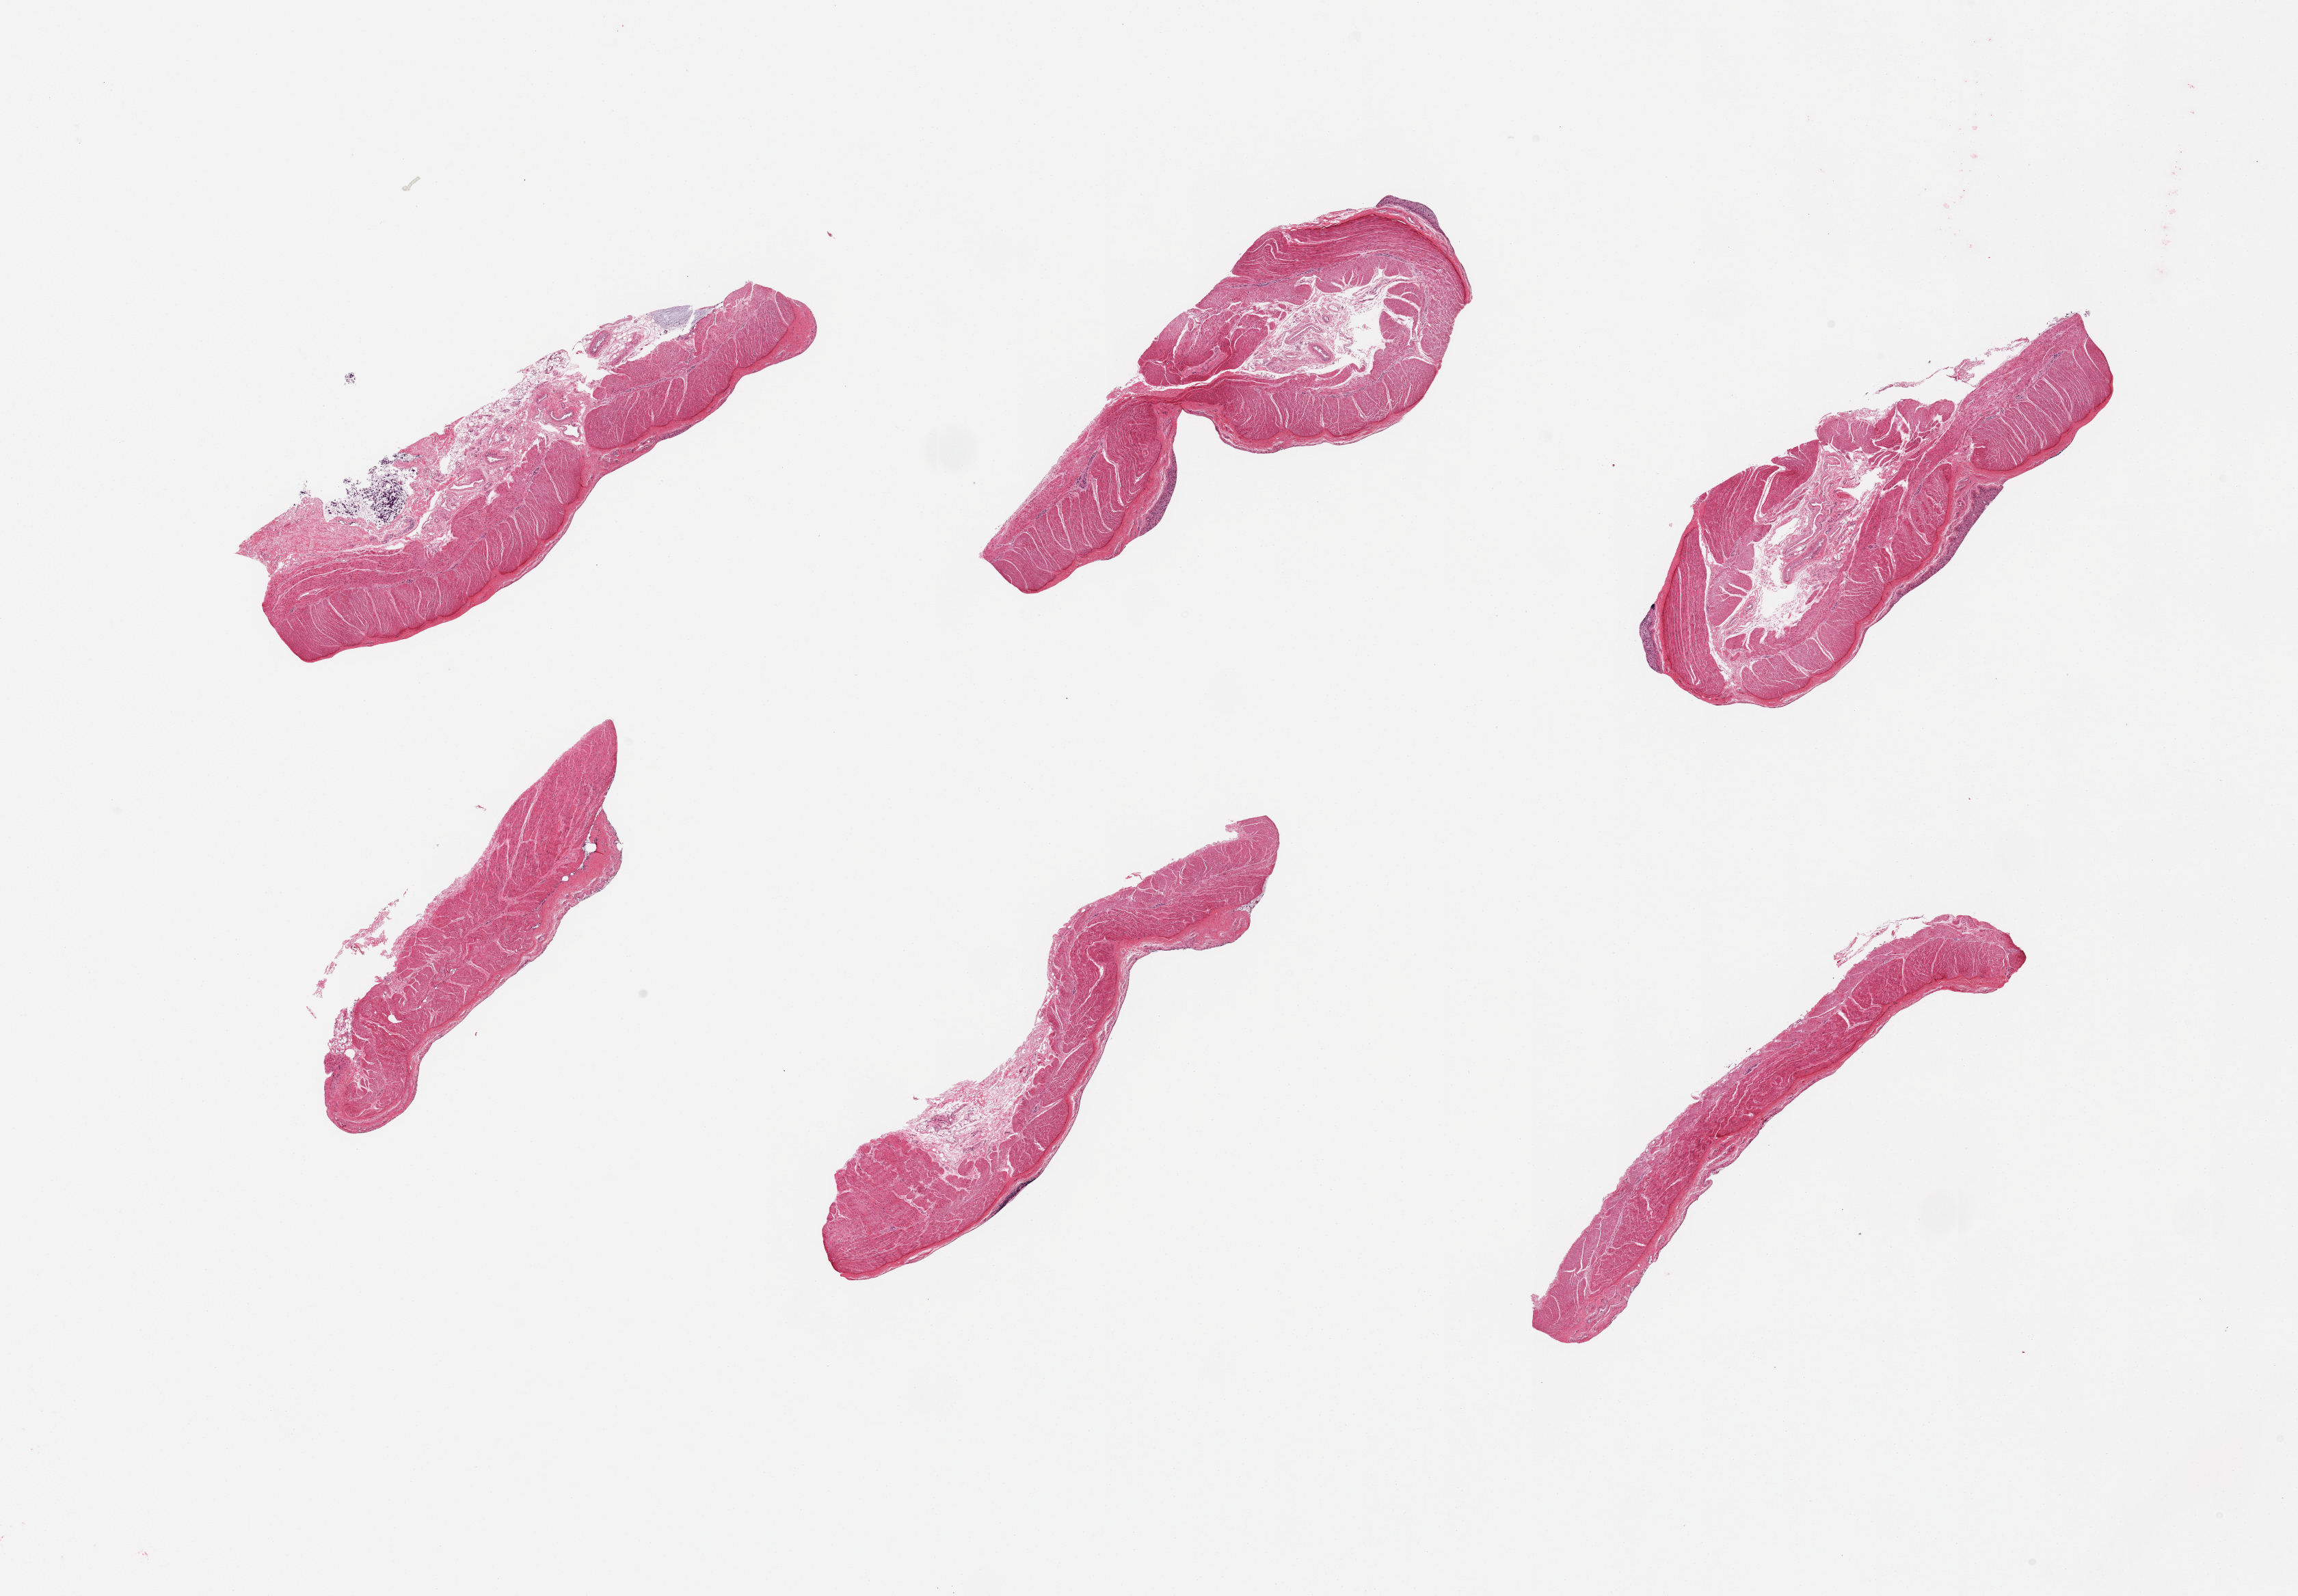
Whole-slide image, haematoxylin and eosin stain, brightfield, shown as a low-resolution overview of the whole scanned area (about 26.6 x 18.5 mm, slide scanned at 20x); PAXgene-fixed paraffin-embedded (PFPE) section; target tissue: sigmoid colon; donor tissue sample. Male donor.
Pathologist's review note for this sample: 6 pieces, 1 with prominent submucosa.